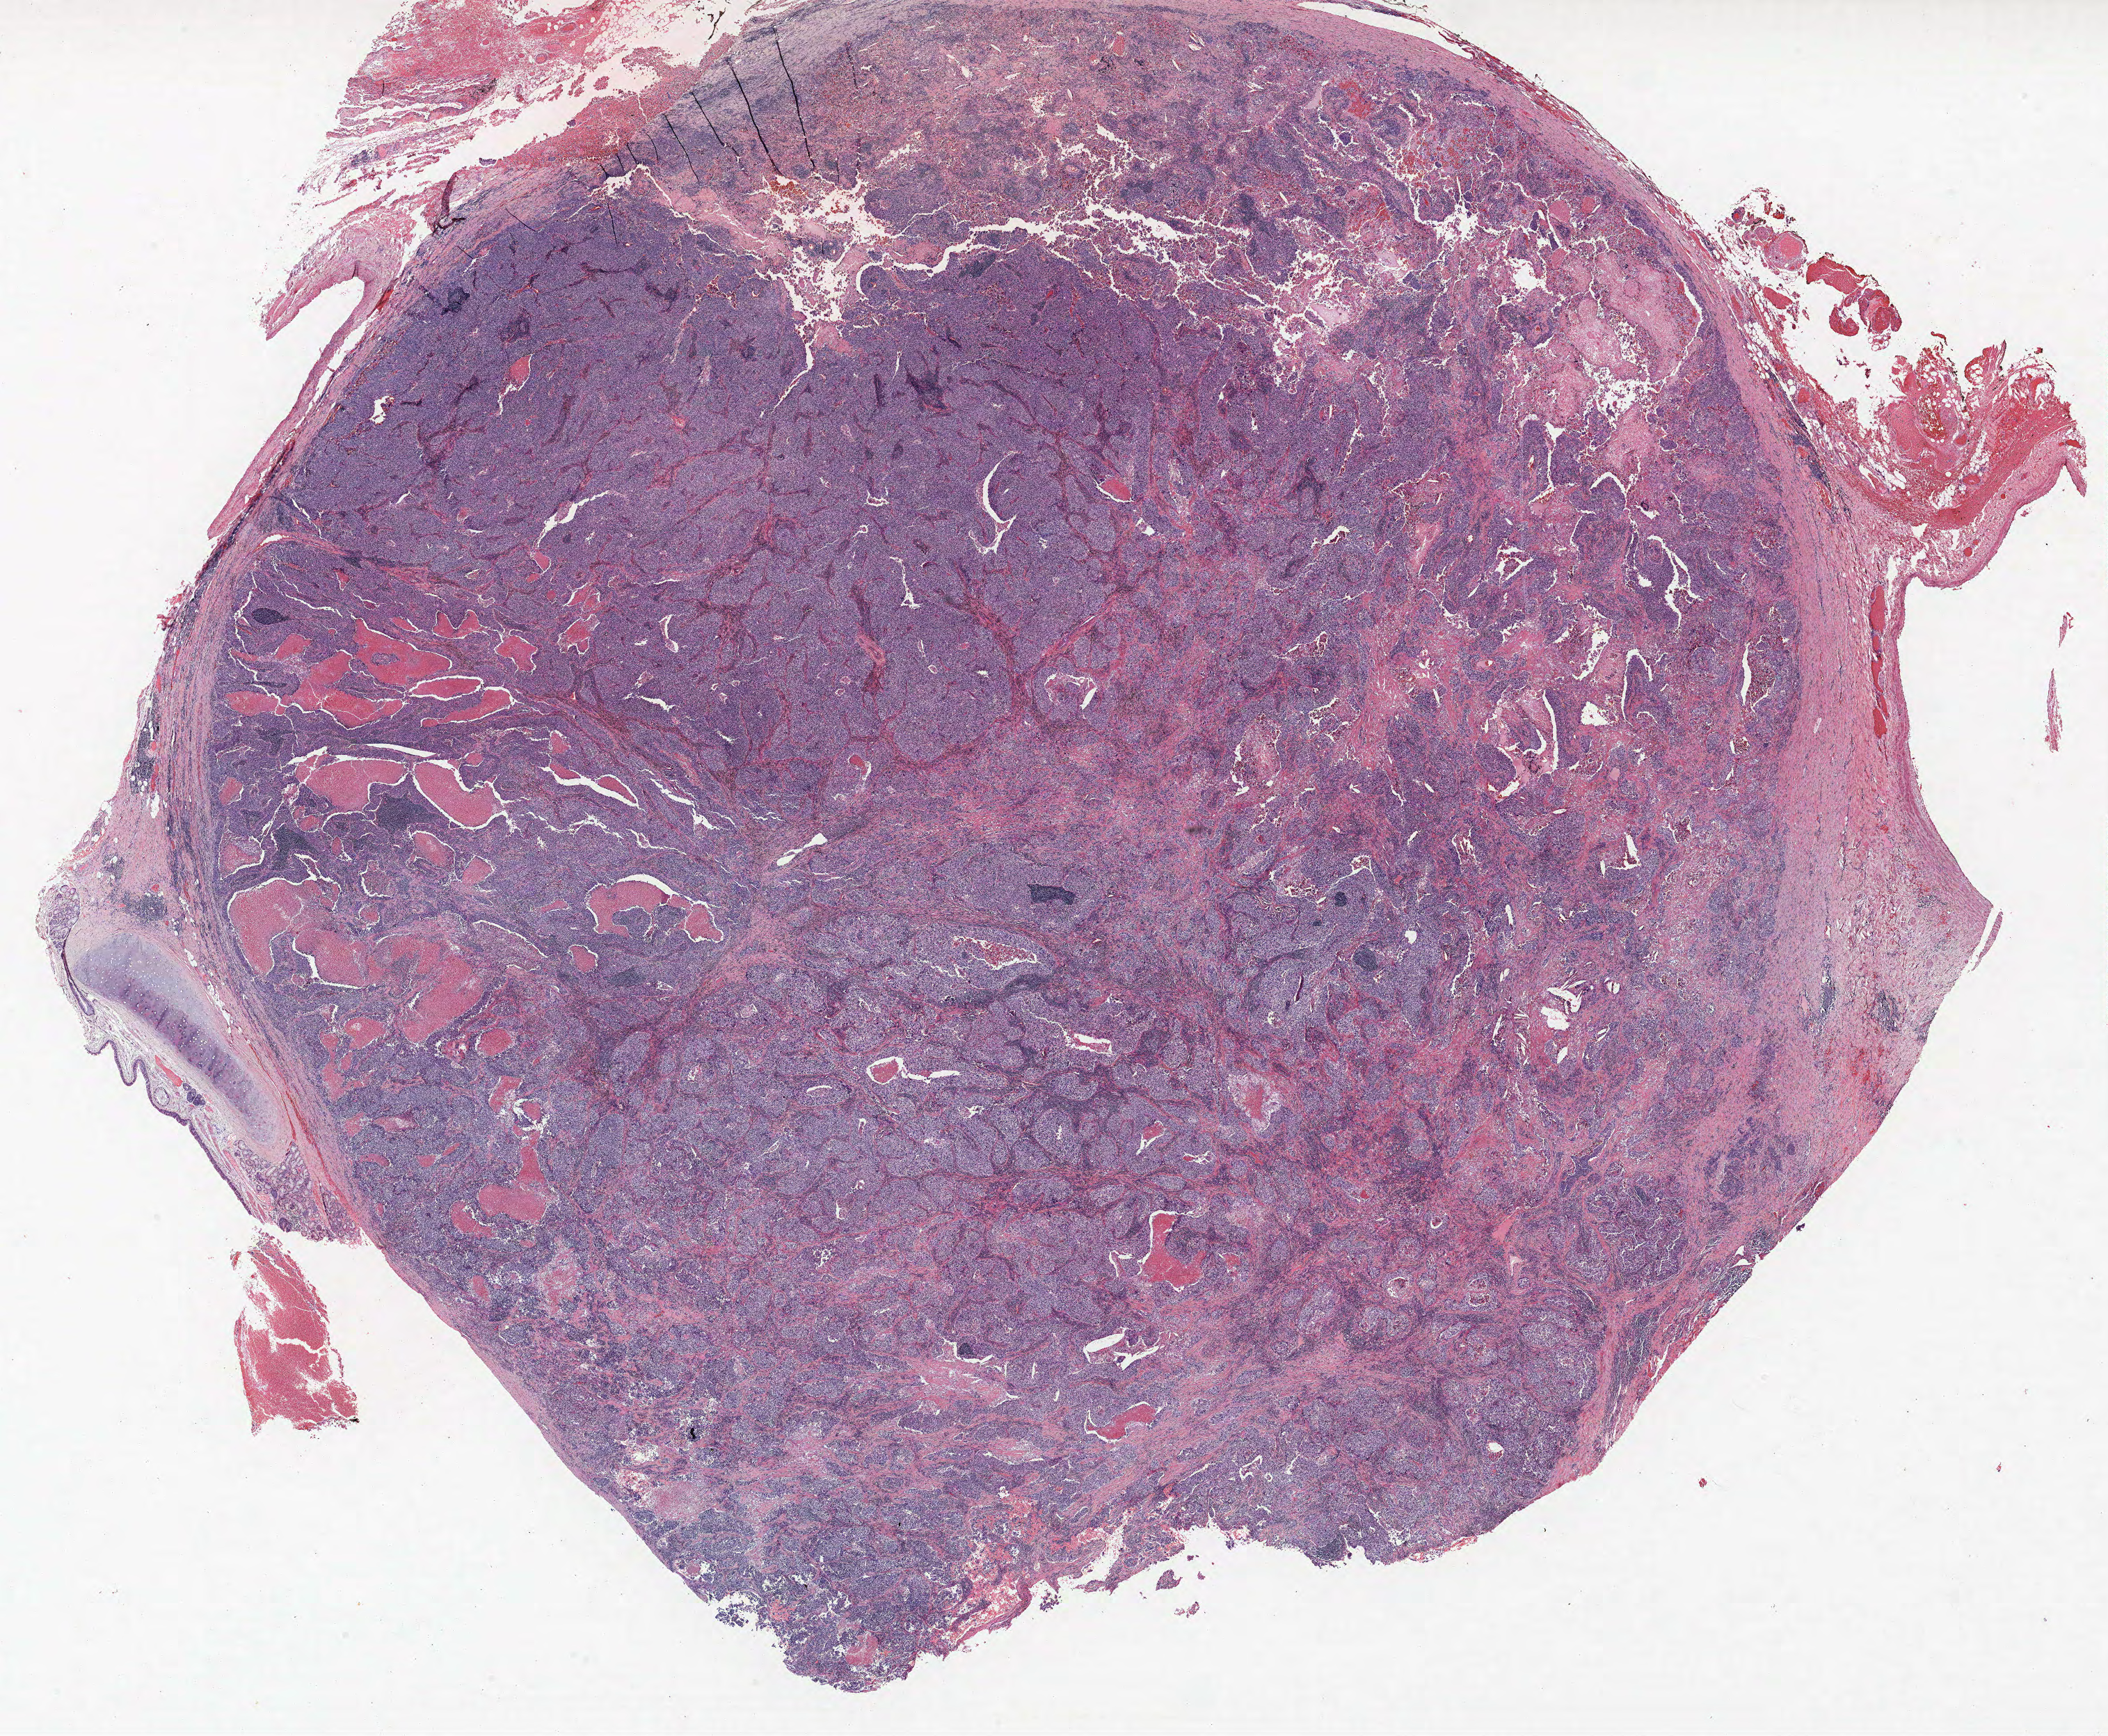
Hematoxylin and eosin (H&E) stained whole-slide image — low-resolution overview of the scanned area, about 24.2 x 20.0 mm; formalin-fixed paraffin-embedded (FFPE) section; lung tissue. Male patient, aged 59 at enrolment. Current smoker at enrolment. Grade: poorly differentiated (G3).
- tumour size (pathology): 9 mm
- stage (AJCC 6th edition): IIA
- primary tumour location (clinical record): left upper lobe
- participant's lung-cancer diagnosis: Squamous cell carcinoma, NOS